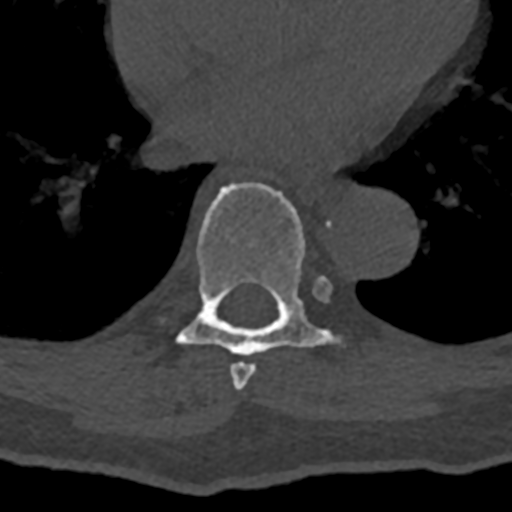
CT including the spine, one axial slice; position 714 of 797 along the scan axis; reconstruction kernel Br40s/3; 120 kVp; bone window (W 1800 / L 400 HU); 0.5 mm slice thickness; 512 × 512 image matrix, field of view 160 × 160 mm. Male patient, age 74 years. From the clinical record (not read from this slice): primary cancer: renal; vertebrae with lytic lesions (as recorded): T10, L1, L2, L3, L4, L5.
Outlined on this slice (semi-automatically segmented with operator editing):
- T7 vertebra: bounding box [x1, y1, x2, y2] px = [230, 279, 326, 390]
- T8 vertebra: [161, 182, 341, 356]